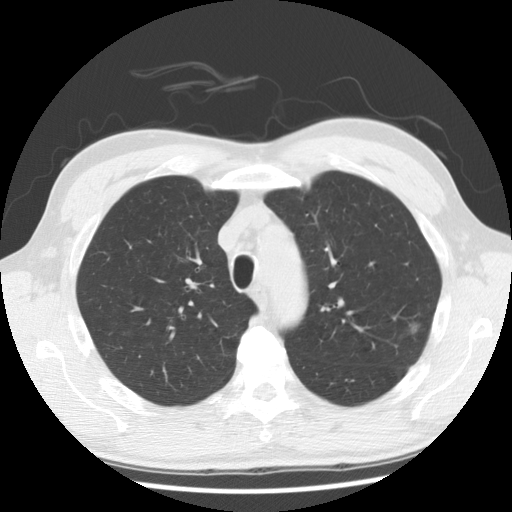
Low-dose screening chest CT, one axial slice; slice 115 of 148 in the series (ordered by position); reconstruction kernel STANDARD; lung window (W 1500 / L -600 HU); 2.5 mm slice thickness; 512 × 512 image matrix, field of view 350 × 350 mm.
Structures marked on this image (outlined manually by an expert reader):
- lesion 1 (tumor, upper lobe of left lung): box from (x=409, y=321) to (x=421, y=335) px